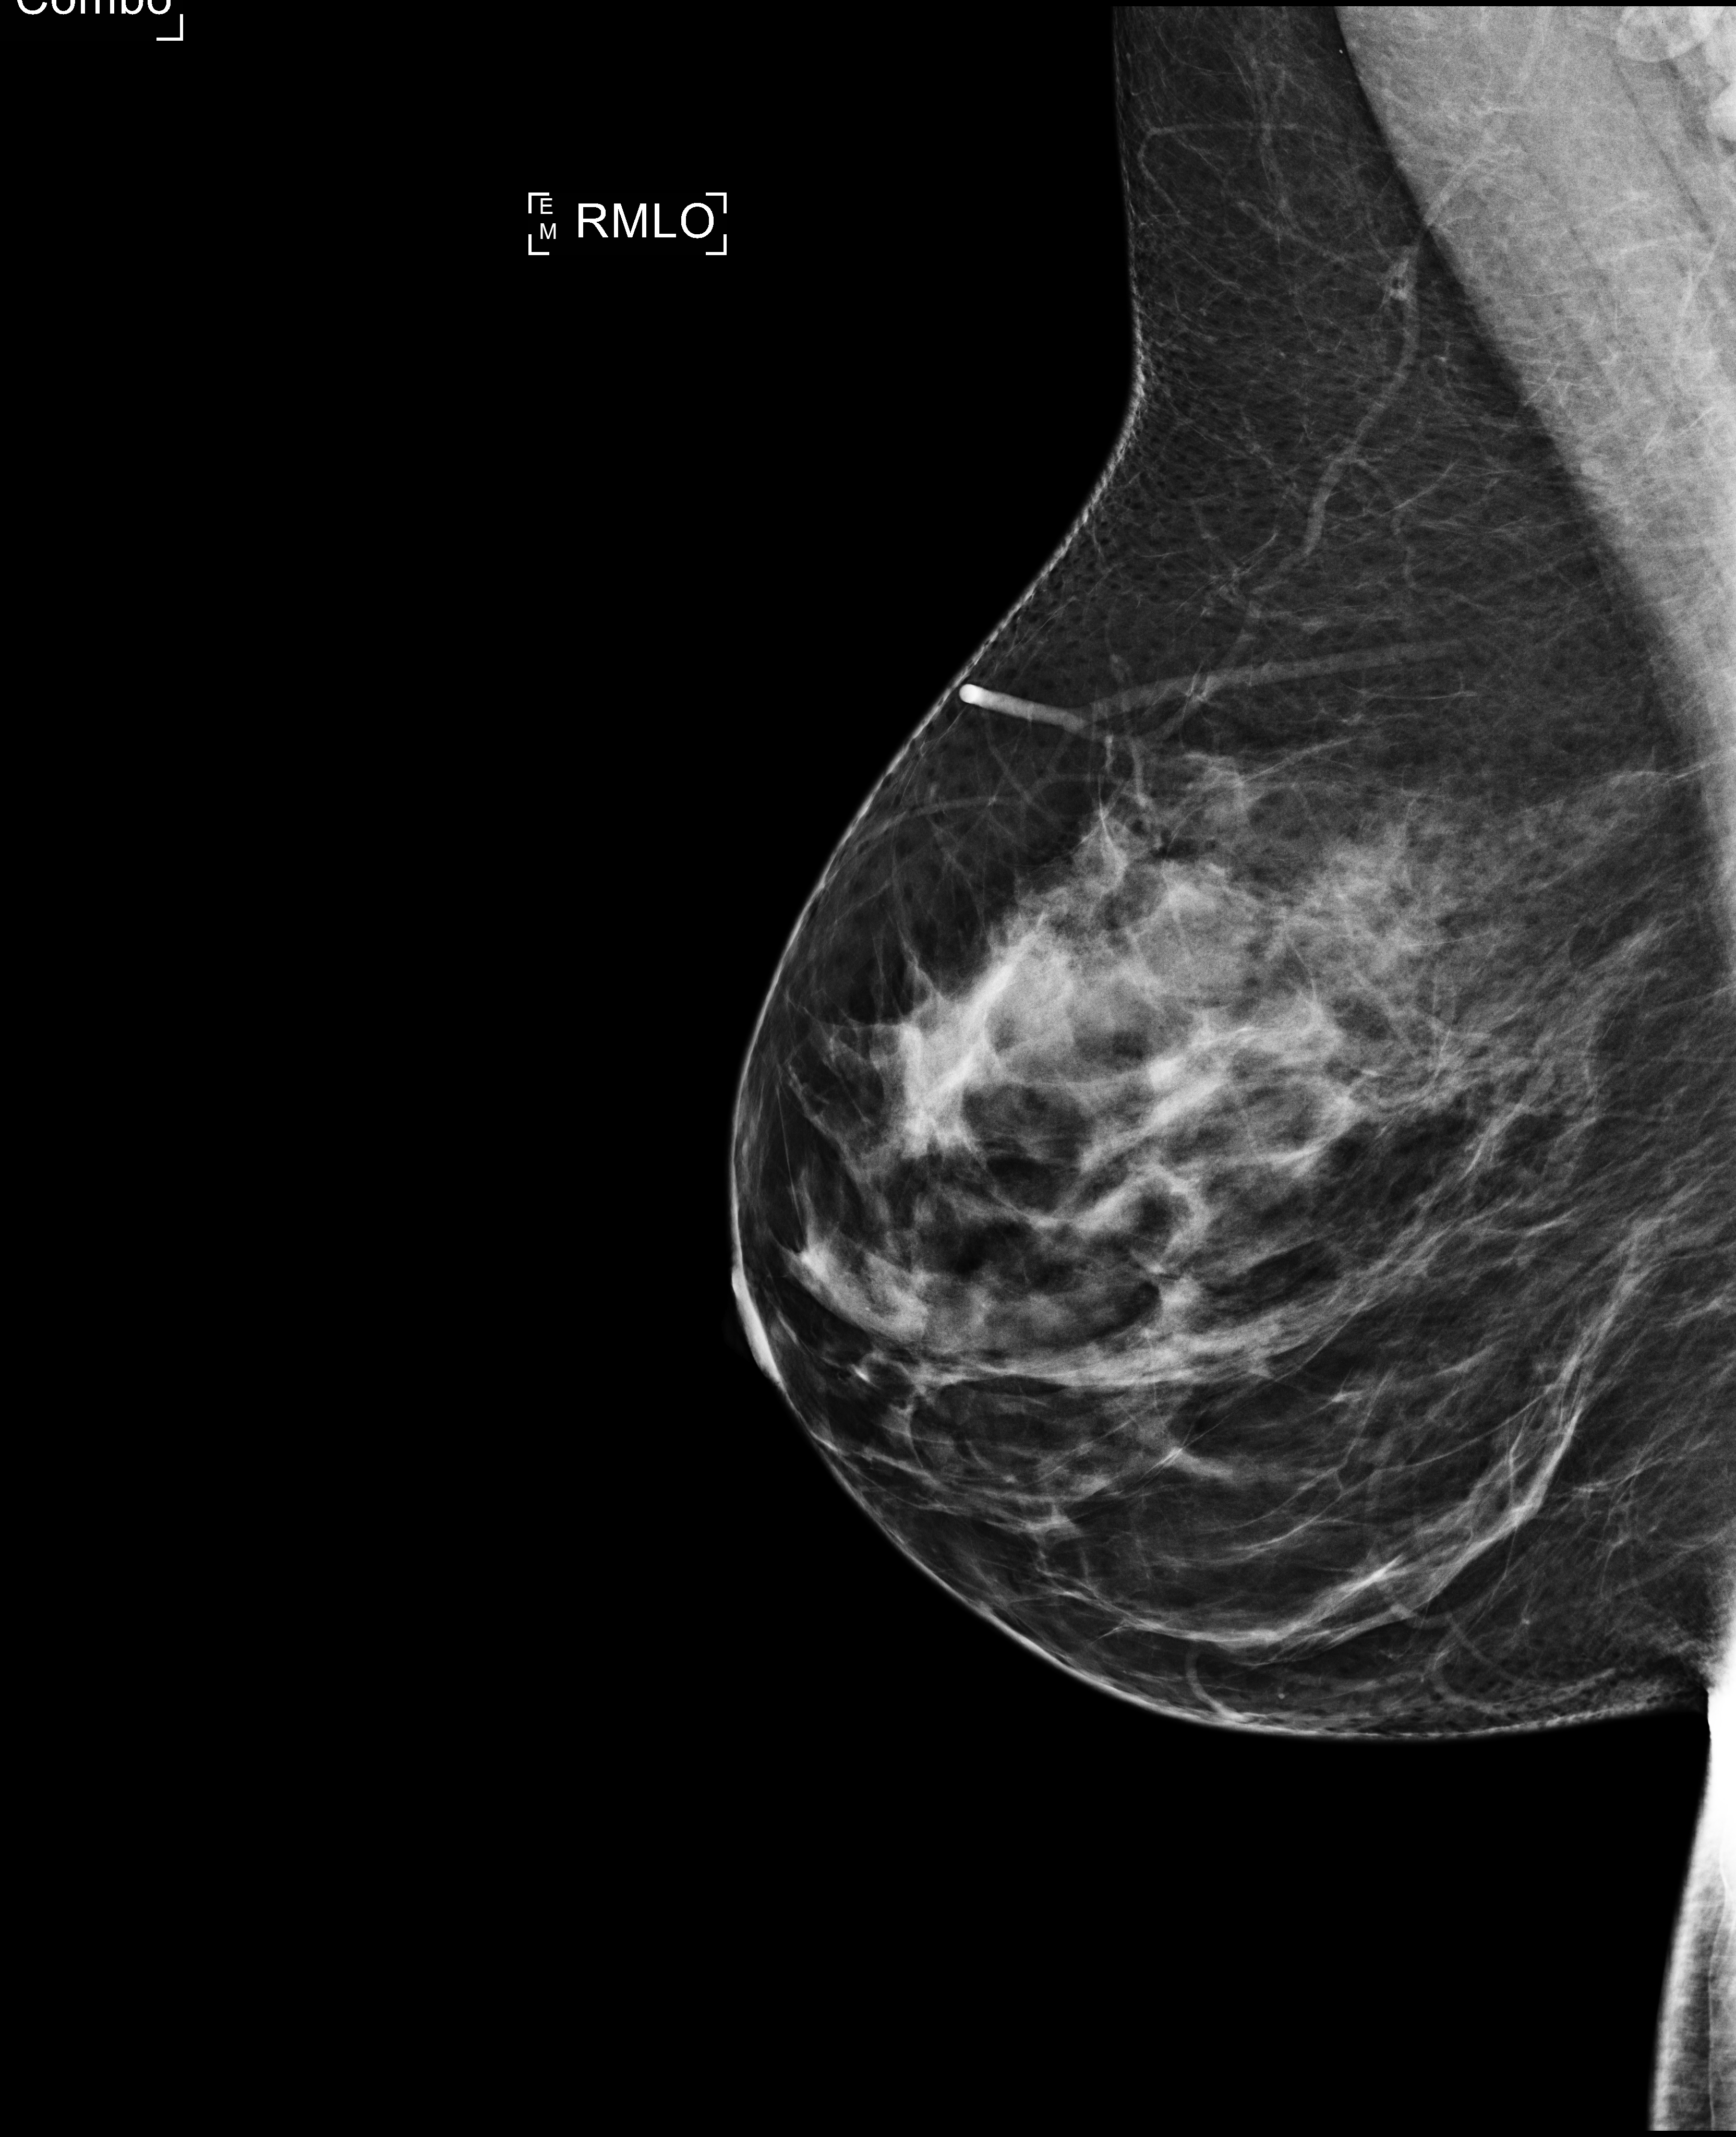
Full-field digital mammogram (FFDM); right breast; mediolateral oblique (MLO) view; annual screening mammography examination; compressed breast thickness 76 mm. Patient: female, 45 years.
- BI-RADS breast density category at the screening exam (both breasts, scale 1–4): 3
- final BI-RADS category for the screening round (tomosynthesis exam, both breasts): category 1
- recall: no recall after this screen